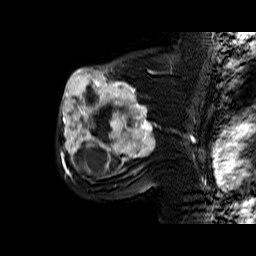
Breast MRI (dynamic contrast-enhanced), one sagittal slice. Slice 41 of 60 in the series (ordered by position). Dynamic contrast-enhanced series, time point 2 of 6 at this slice position (early post-contrast). 1.5 T. TE 6.4 ms, TR 32.9 ms. 4 mm slice thickness. 256 × 256 image matrix, field of view 200 × 200 mm. Female patient. From the clinical record (not read from this slice): setting: breast cancer imaged before/during neoadjuvant chemotherapy; receptor status: triple-negative.
Annotated regions visible in this slice (semi-automatic segmentation, software-assisted and operator-edited):
- analysis volume of interest (the breast-tissue region the enhancement analysis was run in; not a lesion): bounding box <58,65,159,174> (left, top, right, bottom; pixels)
- tumour enhancement mask (voxels above the 100 % enhancement threshold inside the analysis volume of interest): <59,65,156,174>